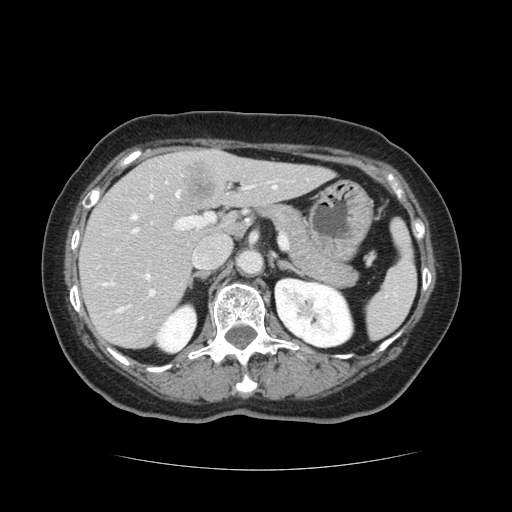
Contrast-enhanced abdominal CT, one axial slice; slice 72 of 128 in the series (ordered by position); intravenous contrast given; soft-tissue window (W 400 / L 40 HU); 2.5 mm slice thickness; 512 × 512 image matrix, field of view 366 × 366 mm. Female patient, age 67 years. From the clinical record (not read from this slice): diagnosis: colorectal cancer liver metastases, imaged before liver resection; multiple liver metastases: yes; largest metastasis: 3 cm.
Annotated regions visible in this slice (expert manual segmentation):
- hepatic veins: bounding box <103,186,277,311> (left, top, right, bottom; pixels)
- liver: <80,149,328,348>
- planned liver remnant (the part of the liver to remain after resection): <80,160,328,348>
- portal vein (with intrahepatic branches): <131,180,278,296>
- liver metastasis: <185,161,212,199>